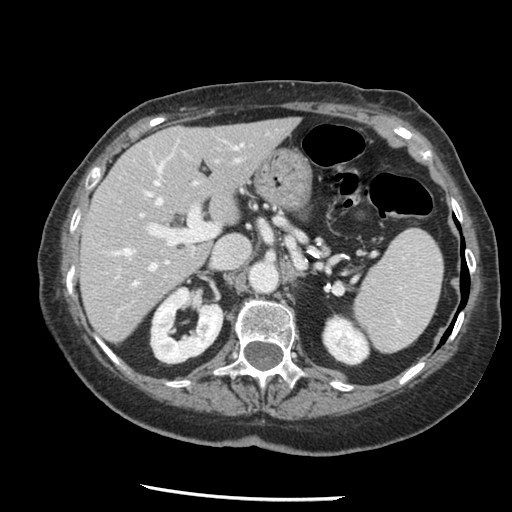
Contrast-enhanced abdominal CT, one axial slice. Slice 82 of 148 in the series (ordered by position). Reconstruction kernel STANDARD. Intravenous contrast given. Soft-tissue window (W 400 / L 40 HU). 512 × 512 image matrix, field of view 330 × 330 mm. Female patient, age 85 years. Case-level facts recorded for this patient, not image findings: diagnosis: colorectal cancer liver metastases, imaged before liver resection; multiple liver metastases: no; largest metastasis: 0.9 cm; disease in both lobes: no.
Outlined on this slice (outlined manually by an expert reader):
- hepatic veins: bounding box (x1, y1, x2, y2) in pixels: (113, 142, 189, 286)
- liver: (81, 119, 298, 341)
- planned liver remnant (the part of the liver to remain after resection): (81, 119, 298, 341)
- portal vein (with intrahepatic branches): (140, 139, 231, 246)